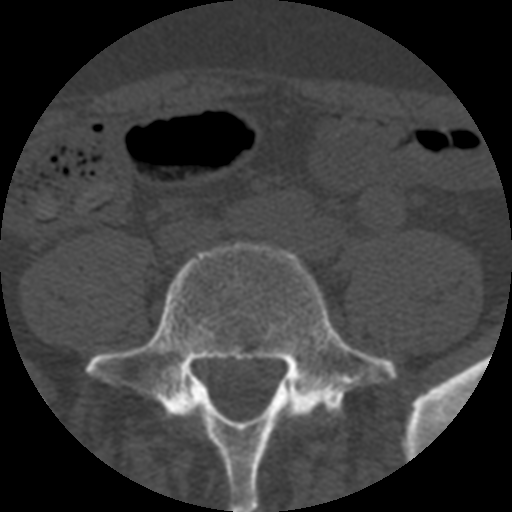
CT including the spine, one axial slice. Position 67 of 508 along the scan axis. Reconstruction kernel STANDARD. 120 kVp. Bone window (W 1800 / L 400 HU). 512 × 512 image matrix. Patient age 57 years. From the clinical record (not read from this slice): primary cancer: prostate.
Annotated regions visible in this slice (semi-automatically segmented with operator editing):
- L5 vertebra: box from (x=85, y=242) to (x=398, y=512) px